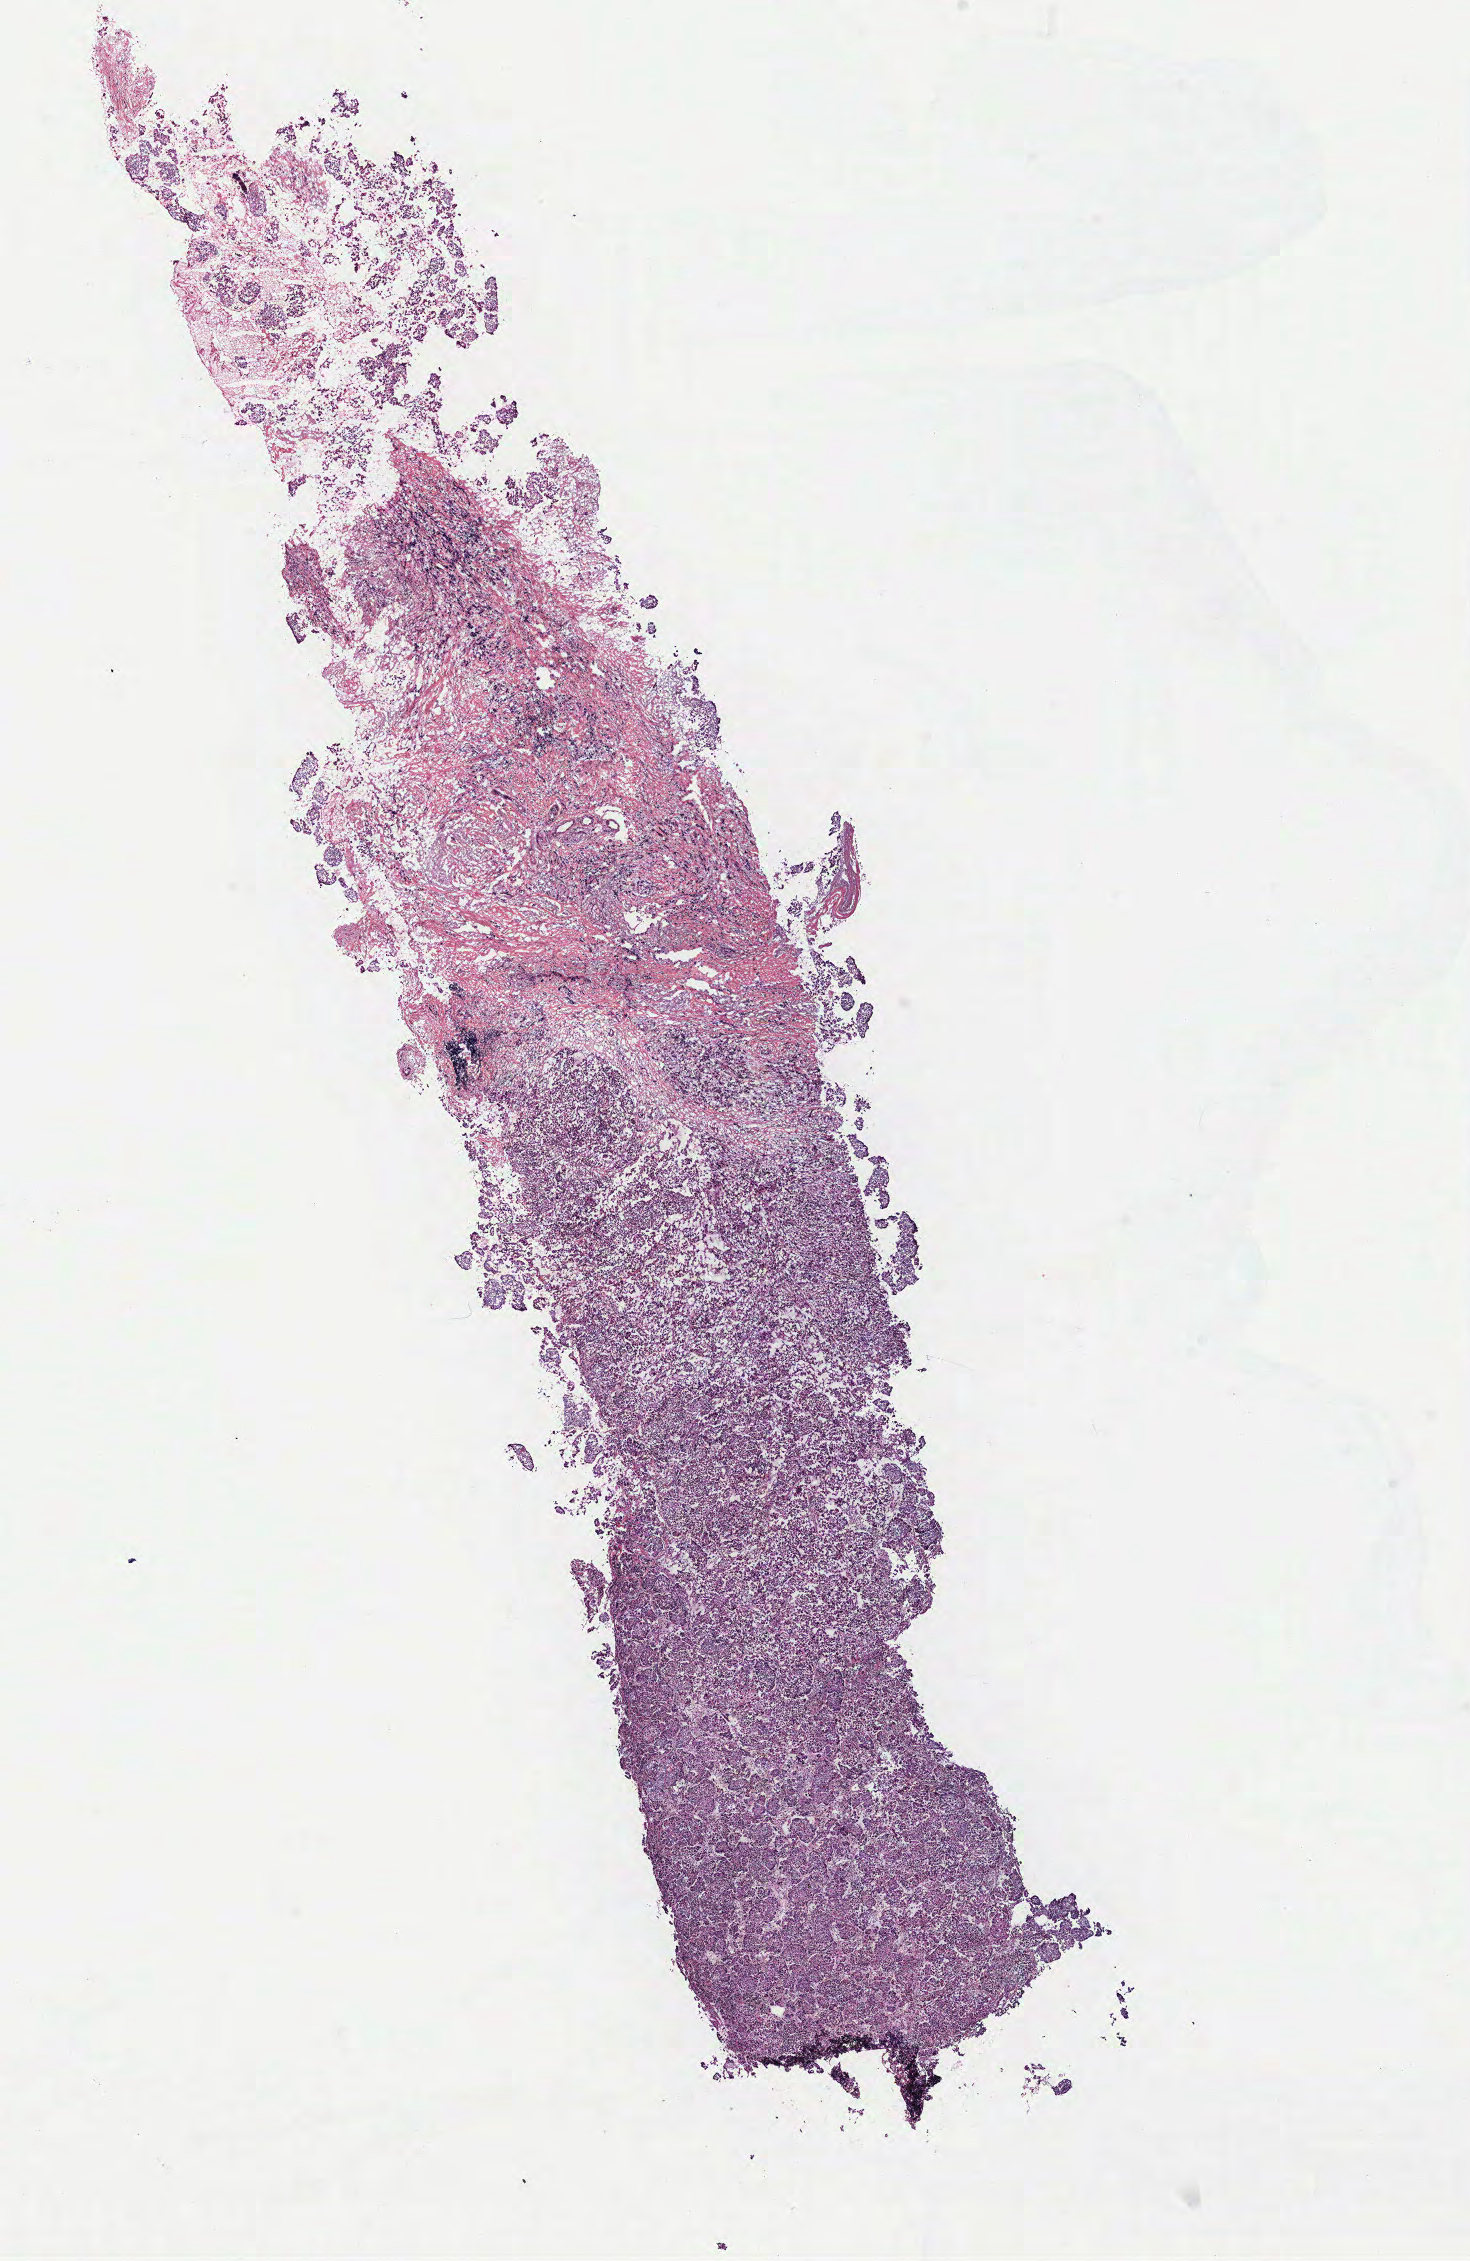
H&E whole-slide image — a low-resolution overview of the entire scanned area, about 11.8 x 18.1 mm. Breast, tissue type not recorded. Patient: female, age 61 years.
* patient diagnosis: Infiltrating duct carcinoma, NOS